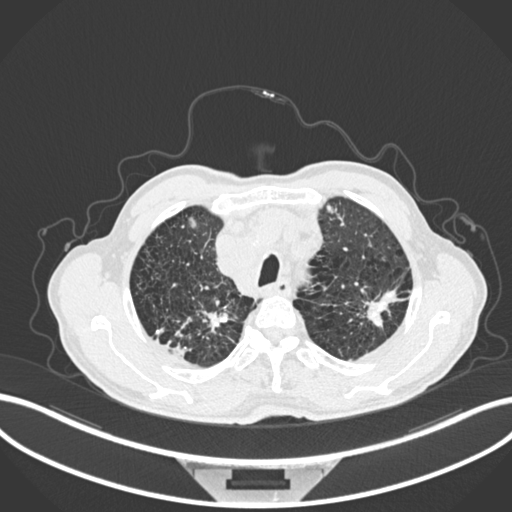
Chest CT, one axial slice. Position 228 of 287 along the scan axis. Reconstruction kernel B30f. 120 kVp. Lung window (W 1500 / L -600 HU). 1 mm slice thickness. 512 × 512 image matrix, field of view 400 × 400 mm. Patient: male, 74 years. Case-level facts recorded for this patient, not image findings: clinical TNM (as recorded): T2a N1 M0.
Outlined on this slice (rectangle marked by the reading radiologist):
- lung tumour (recorded histology: adenocarcinoma): bounding box [x1, y1, x2, y2] px = [360, 283, 398, 333]